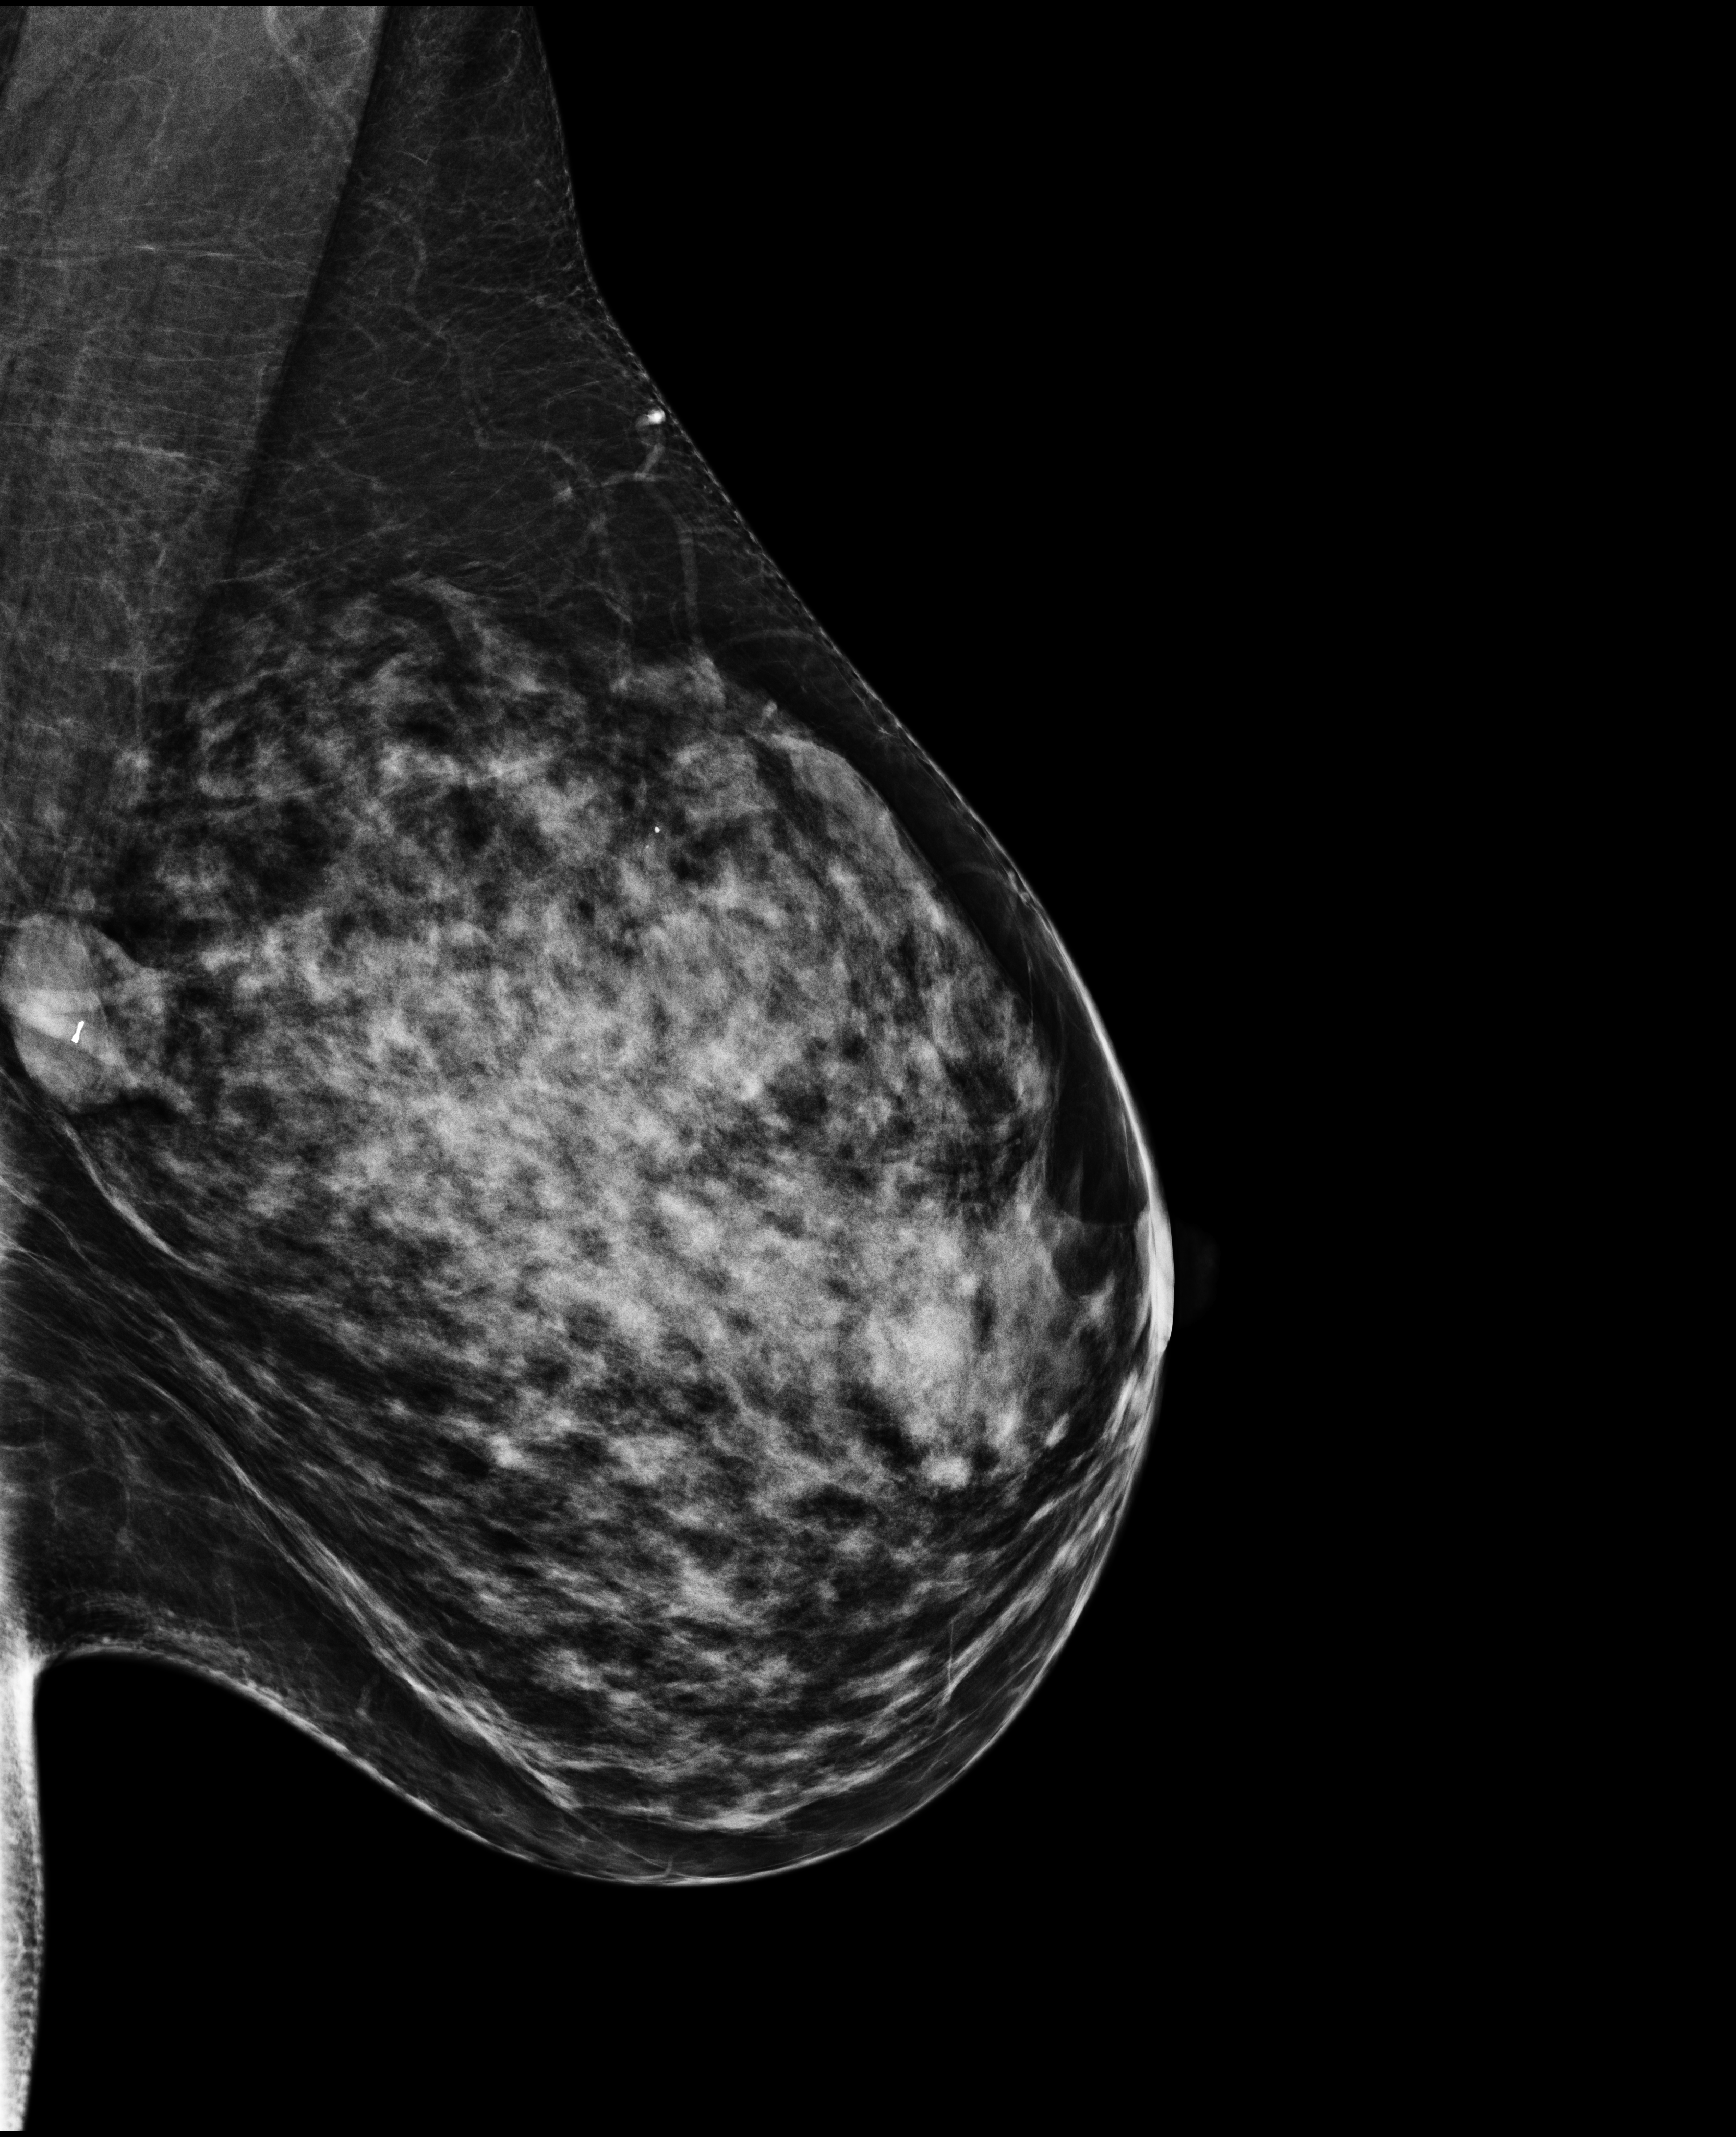
Screening examination. Patient aged 45 years (female).
Image type: full-field digital mammogram. Breast: left. Projection: MLO view.